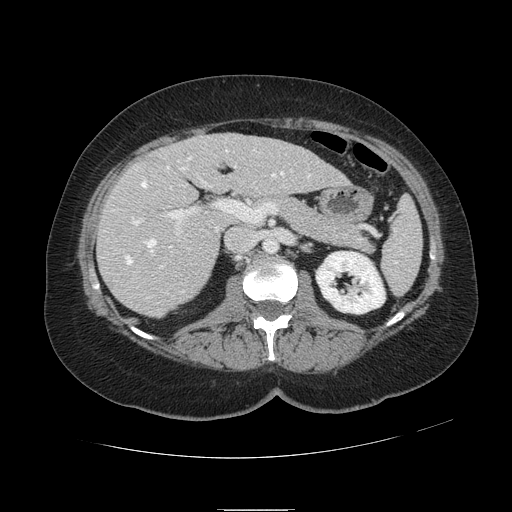
Contrast-enhanced abdominal CT, one axial slice; position 51 of 121 along the scan axis; 120 kVp; soft-tissue window (W 400 / L 40 HU); 512 × 512 image matrix, field of view 400 × 400 mm. Female patient, age 52 years. Case-level facts recorded for this patient, not image findings: diagnosis: colorectal cancer liver metastases, imaged before liver resection; multiple liver metastases: yes; largest metastasis: 6.3 cm; disease in both lobes: no.
Outlined on this slice (manually delineated by an expert):
- hepatic veins: box from (x=125, y=150) to (x=310, y=292) px
- liver: (x=99, y=134)–(x=346, y=316)
- planned liver remnant (the part of the liver to remain after resection): (x=172, y=134)–(x=347, y=196)
- portal vein (with intrahepatic branches): (x=132, y=166)–(x=293, y=268)